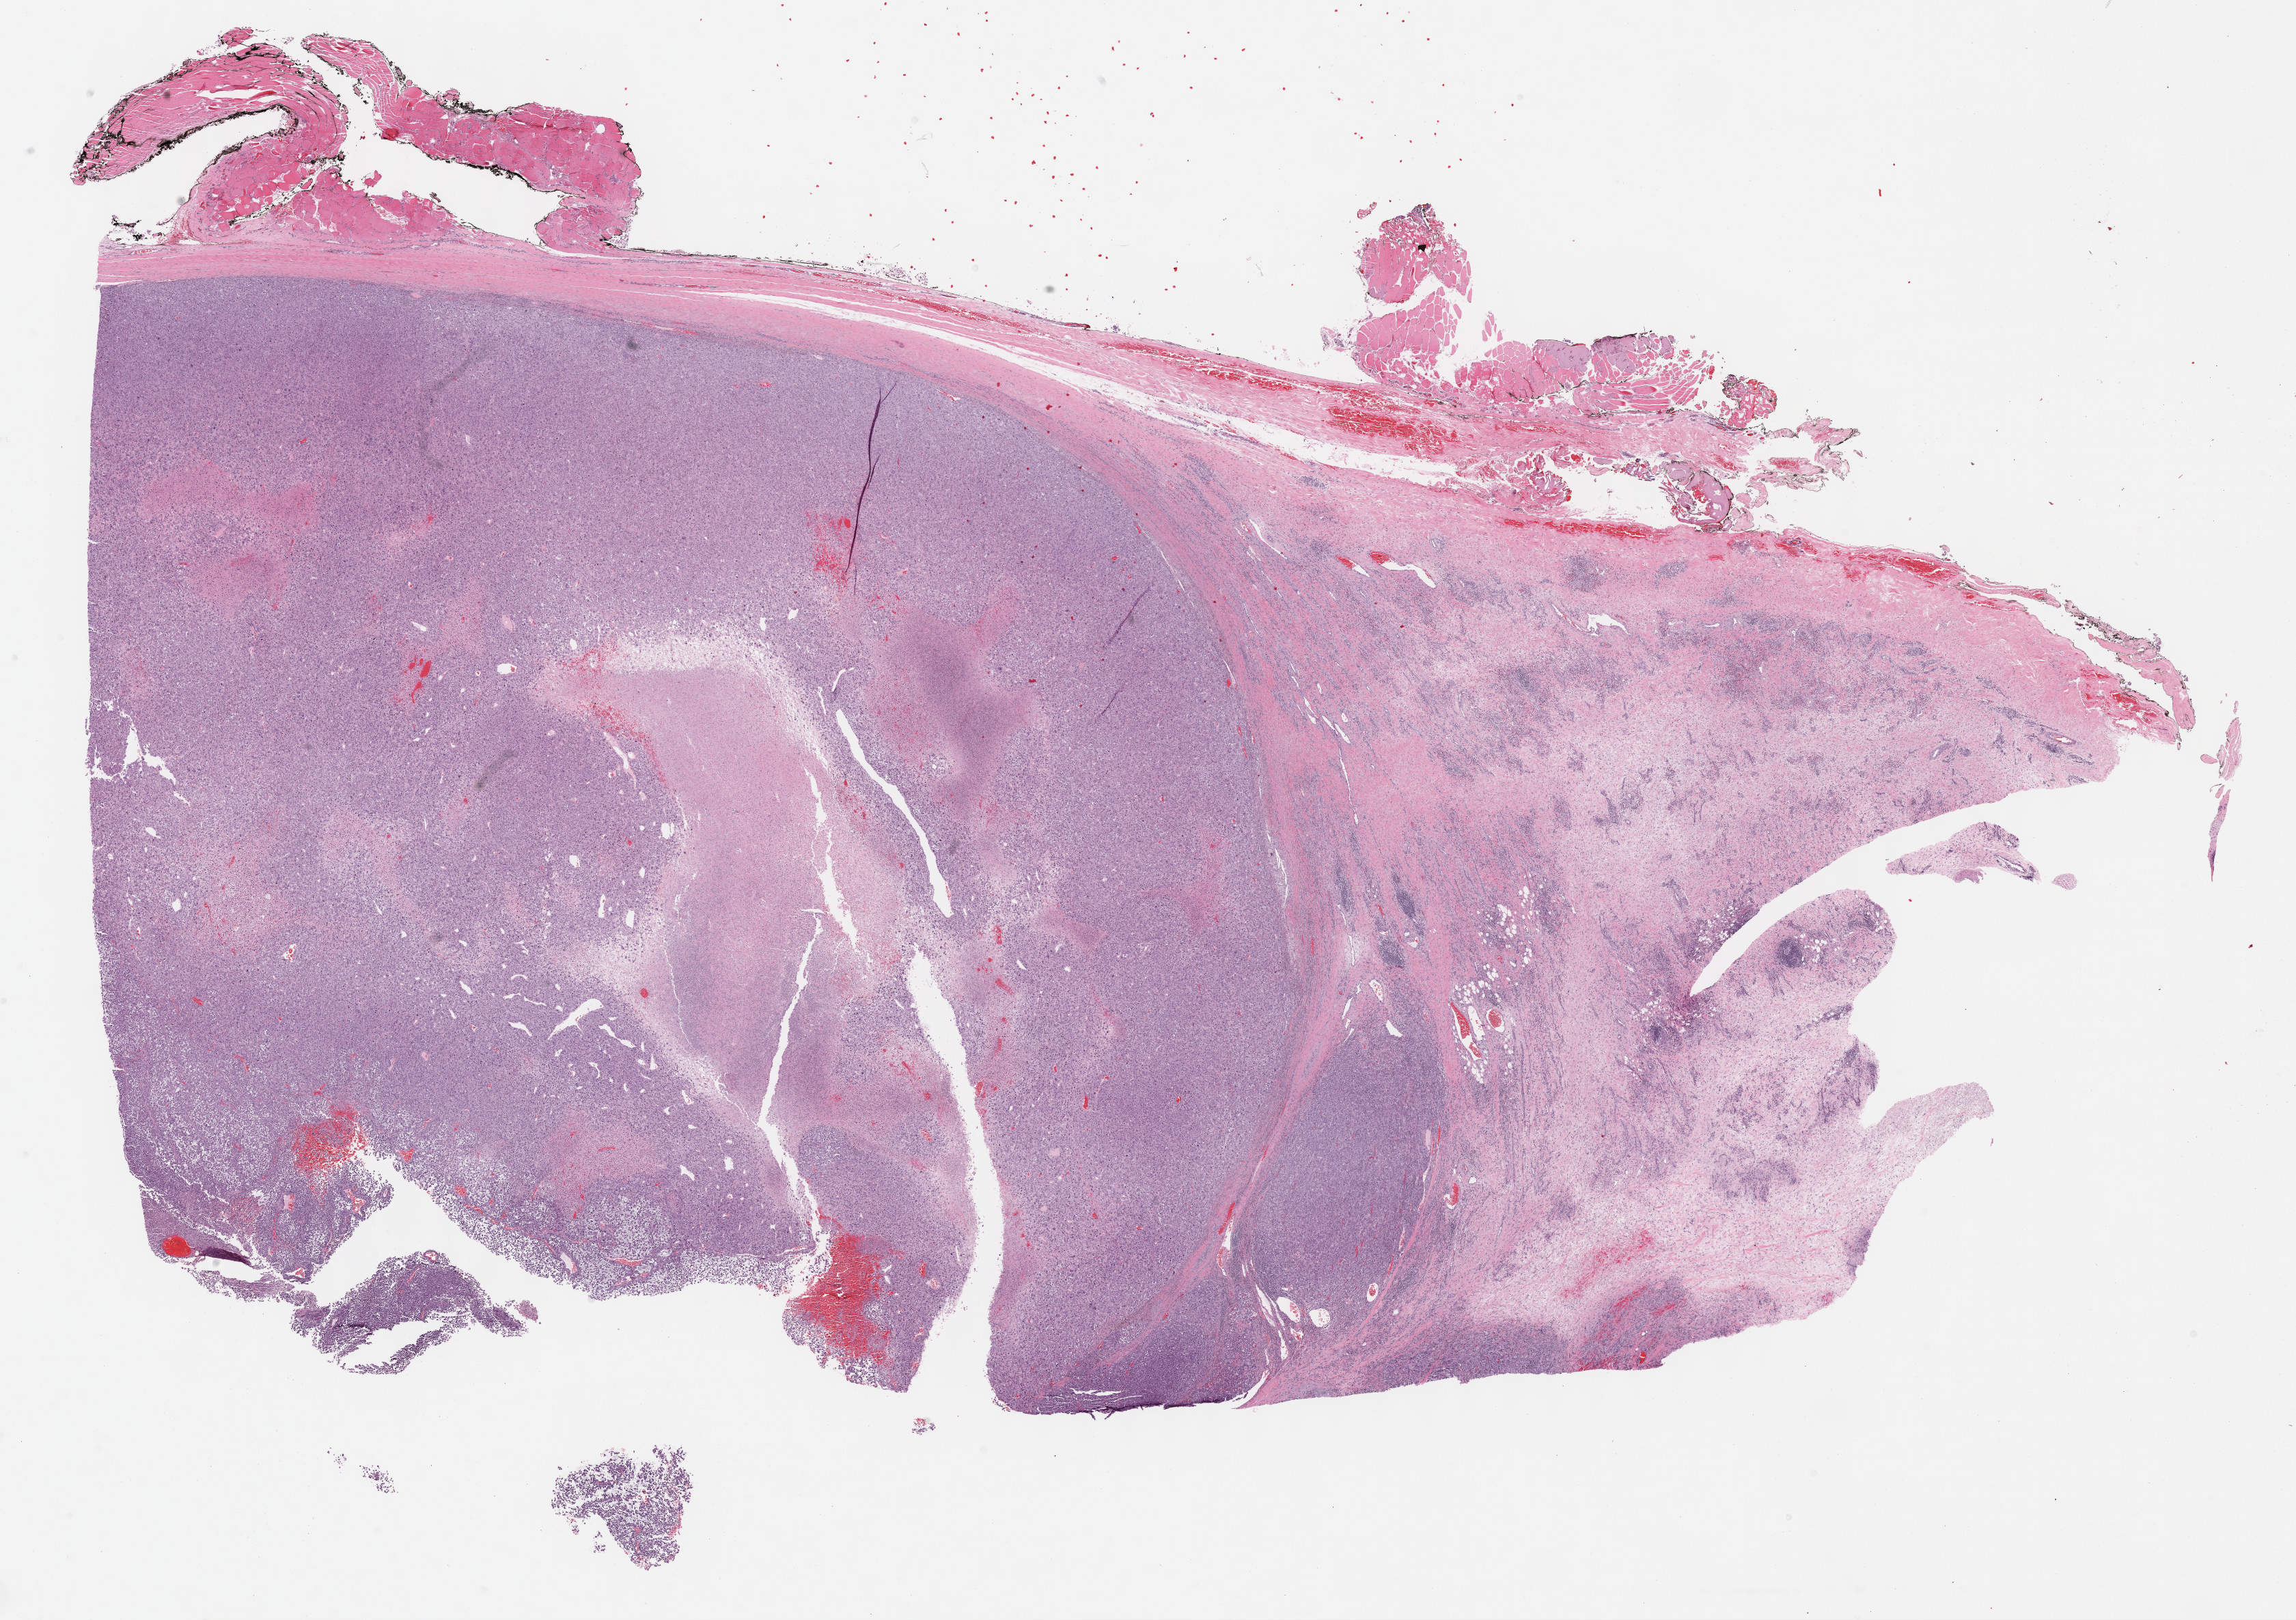
Whole-slide histology image, H&E-stained — a low-resolution overview of the entire scanned area, about 27.2 x 19.2 mm (from a 40x scan); FFPE section; primary tumour sample from the connective, subcutaneous and other soft tissues. Patient: female, age at initial diagnosis 73 years.
- diagnosis: Undifferentiated sarcoma (connective, subcutaneous and other soft tissues of lower limb and hip)